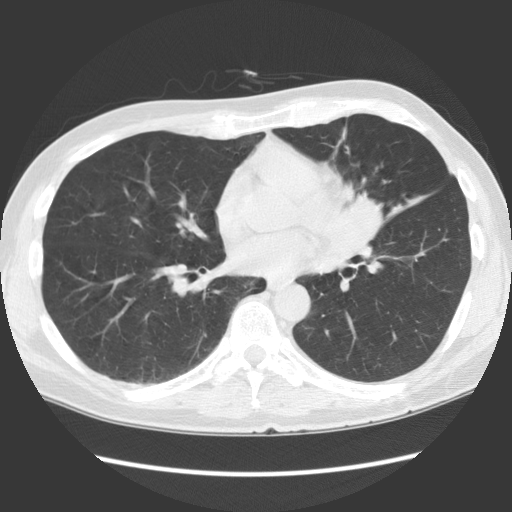
Low-dose screening chest CT, one axial slice; position 63 of 136 along the scan axis; reconstruction kernel STANDARD; 140 kVp; lung window (W 1500 / L -600 HU); 2.5 mm slice thickness; 512 × 512 image matrix, field of view 360 × 360 mm.
Structures marked on this image (manually delineated by an expert):
- lesion 1 (tumor, hilum of left lung): bounding box (x1, y1, x2, y2) in pixels: (342, 192, 383, 240)